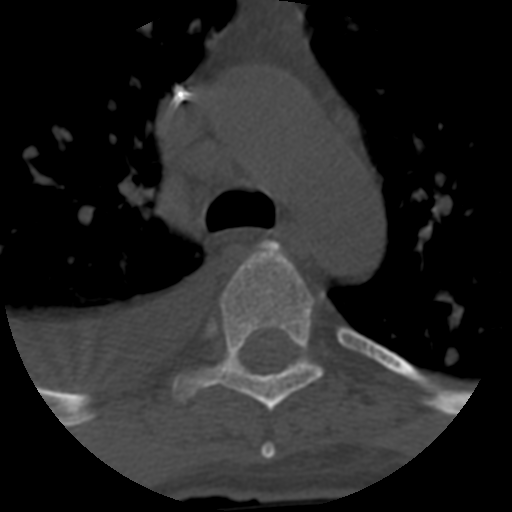
CT including the spine, one axial slice. Position 455 of 708 along the scan axis. 120 kVp. One of 3 acquisitions stored at this slice position. Bone window (W 1800 / L 400 HU). 512 × 512 image matrix. Patient age 55 years. Case-level facts recorded for this patient, not image findings: primary cancer: colon.
Outlined on this slice (semi-automatic segmentation, software-assisted and operator-edited):
- T4 vertebra: bounding box <261,444,276,459> (left, top, right, bottom; pixels)
- T5 vertebra: <171,241,322,412>